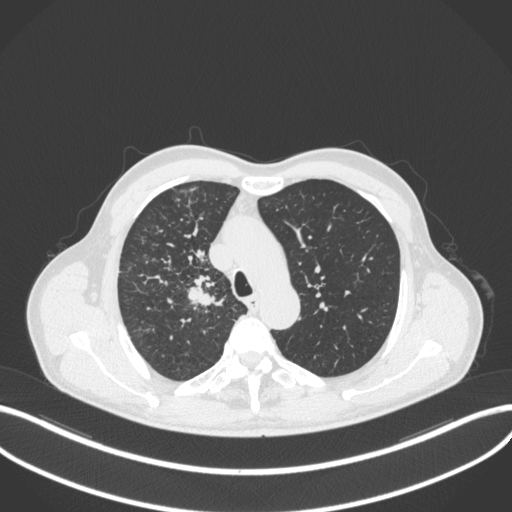
Chest CT, one axial slice. Reconstruction kernel B31f. Lung window (W 1500 / L -600 HU). 512 × 512 image matrix, field of view 400 × 400 mm. Patient: male, 69 years. From the clinical record (not read from this slice): clinical TNM (as recorded): T2a N0 M0.
Annotated regions visible in this slice (bounding box drawn by a radiologist):
- lung tumour (recorded histology: adenocarcinoma): box from (x=180, y=273) to (x=223, y=312) px